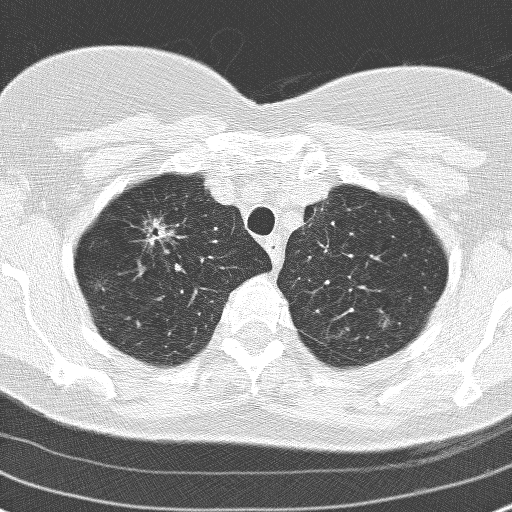
Axial slice from a low-dose chest CT screening exam; second screening round (one year after baseline); lung window (W 1500 / L -600 HU); slice 31 of 160 in the series. Female participant, aged 60 years at enrolment. Former smoker at enrolment.
Lesion marked by an expert reader, bounding box (x1, y1, x2, y2) in pixels: (126, 207, 180, 258). Reader record for this screening exam (exam-level; its link to the box is not recorded): non-calcified nodule or mass ≥4 mm, right upper lobe, 17 × 15 mm, spiculated (stellate) margins, soft tissue attenuation, pre-existing on the prior screen: yes; interval growth: yes. Later outcome: lung cancer diagnosed 78 days after this screen — adenocarcinoma, NOS, right upper lobe, moderately differentiated (G2), stage IA (AJCC 6th edition), 23 mm at pathology.